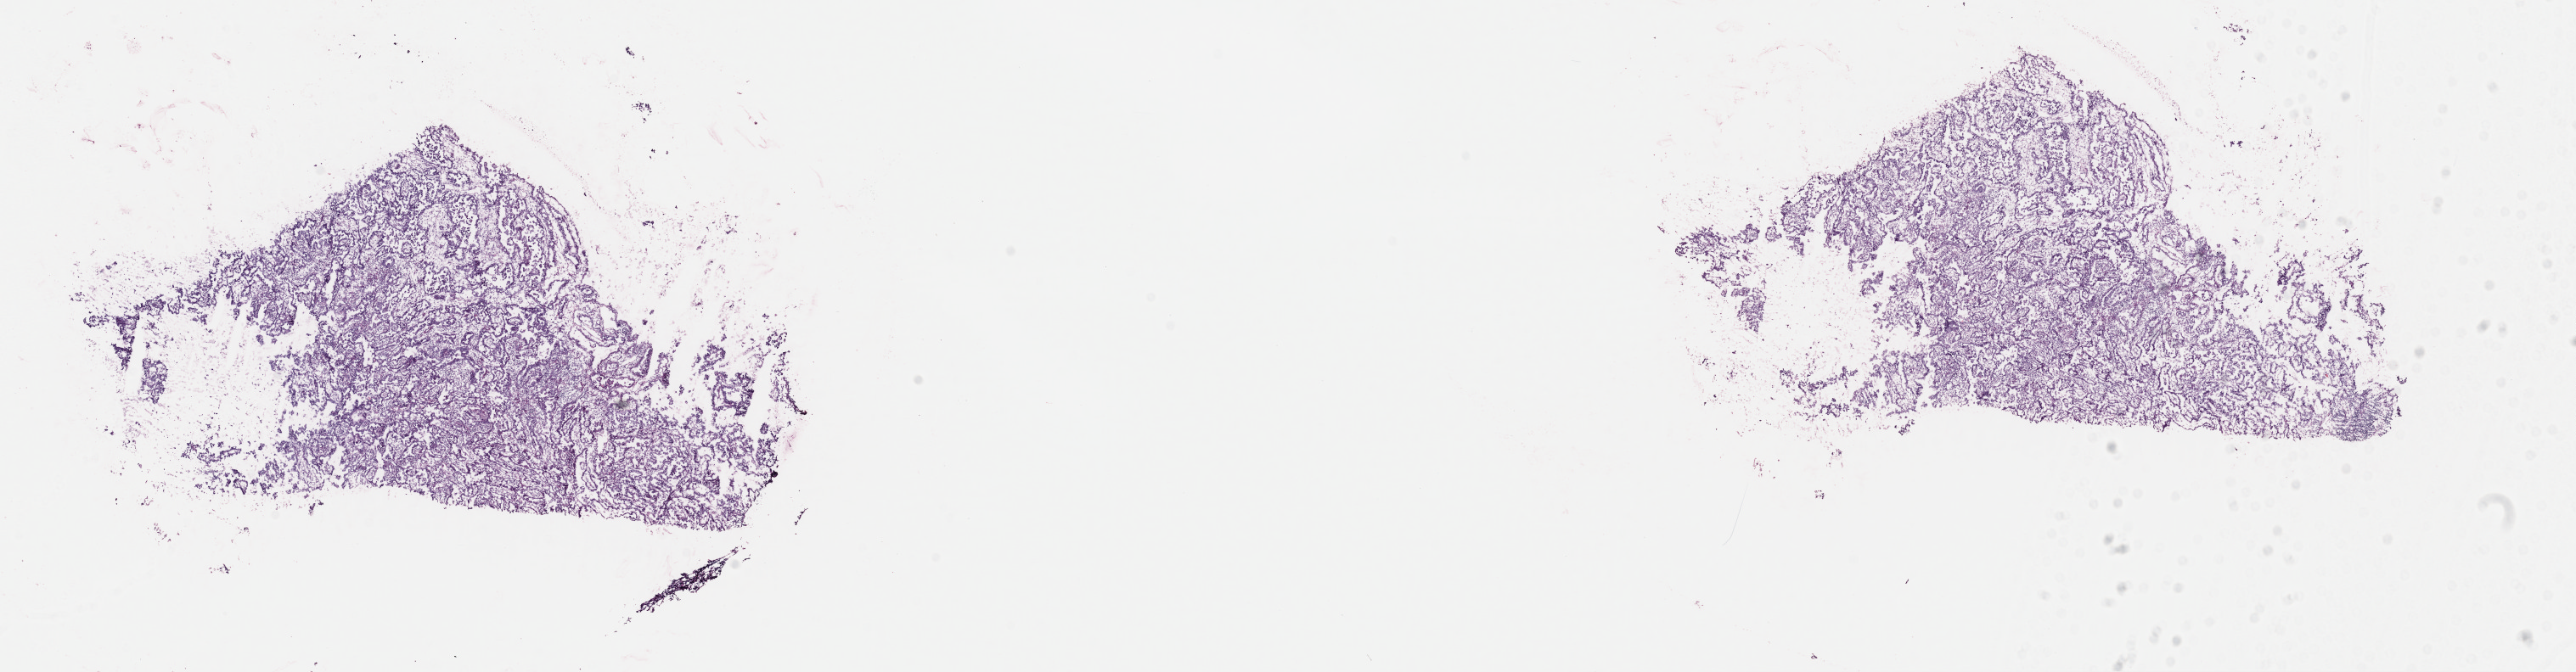
H&E-stained whole-slide image — a low-resolution overview of the entire scanned area, about 24.0 x 6.3 mm; frozen section; uterus, primary tumour sample. Female, age 69 years at initial diagnosis. Histologic grade: G3 (poorly differentiated). Slide review estimates, as recorded: tumour cells 85%, tumour nuclei 75%, normal cells 0%, stromal cells 10%, necrosis 5%. Infiltration values recorded for this section: lymphocyte infiltration 10%, monocyte infiltration 4%, neutrophil infiltration 1%.
Histologic diagnosis: Serous cystadenocarcinoma, NOS (endometrium). FIGO stage: IIIA.